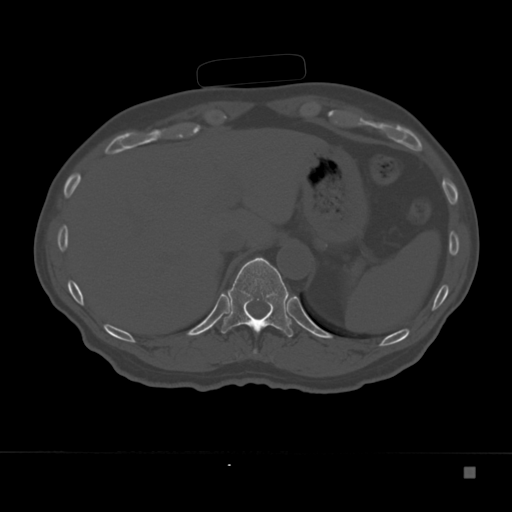
CT including the spine, one axial slice. Slice 155 of 332 in the series (ordered by position). Reconstruction kernel Br40s. 120 kVp. Bone window (W 1800 / L 400 HU). 1.5 mm slice thickness. 512 × 512 image matrix, field of view 389 × 389 mm. Patient: male, 72 years. Case-level facts recorded for this patient, not image findings: primary cancer: skeletal.
Structures marked on this image (semi-automatic segmentation, software-assisted and operator-edited):
- T10 vertebra: bounding box (x1, y1, x2, y2) in pixels: (253, 349, 257, 354)
- T11 vertebra: (221, 257, 293, 337)